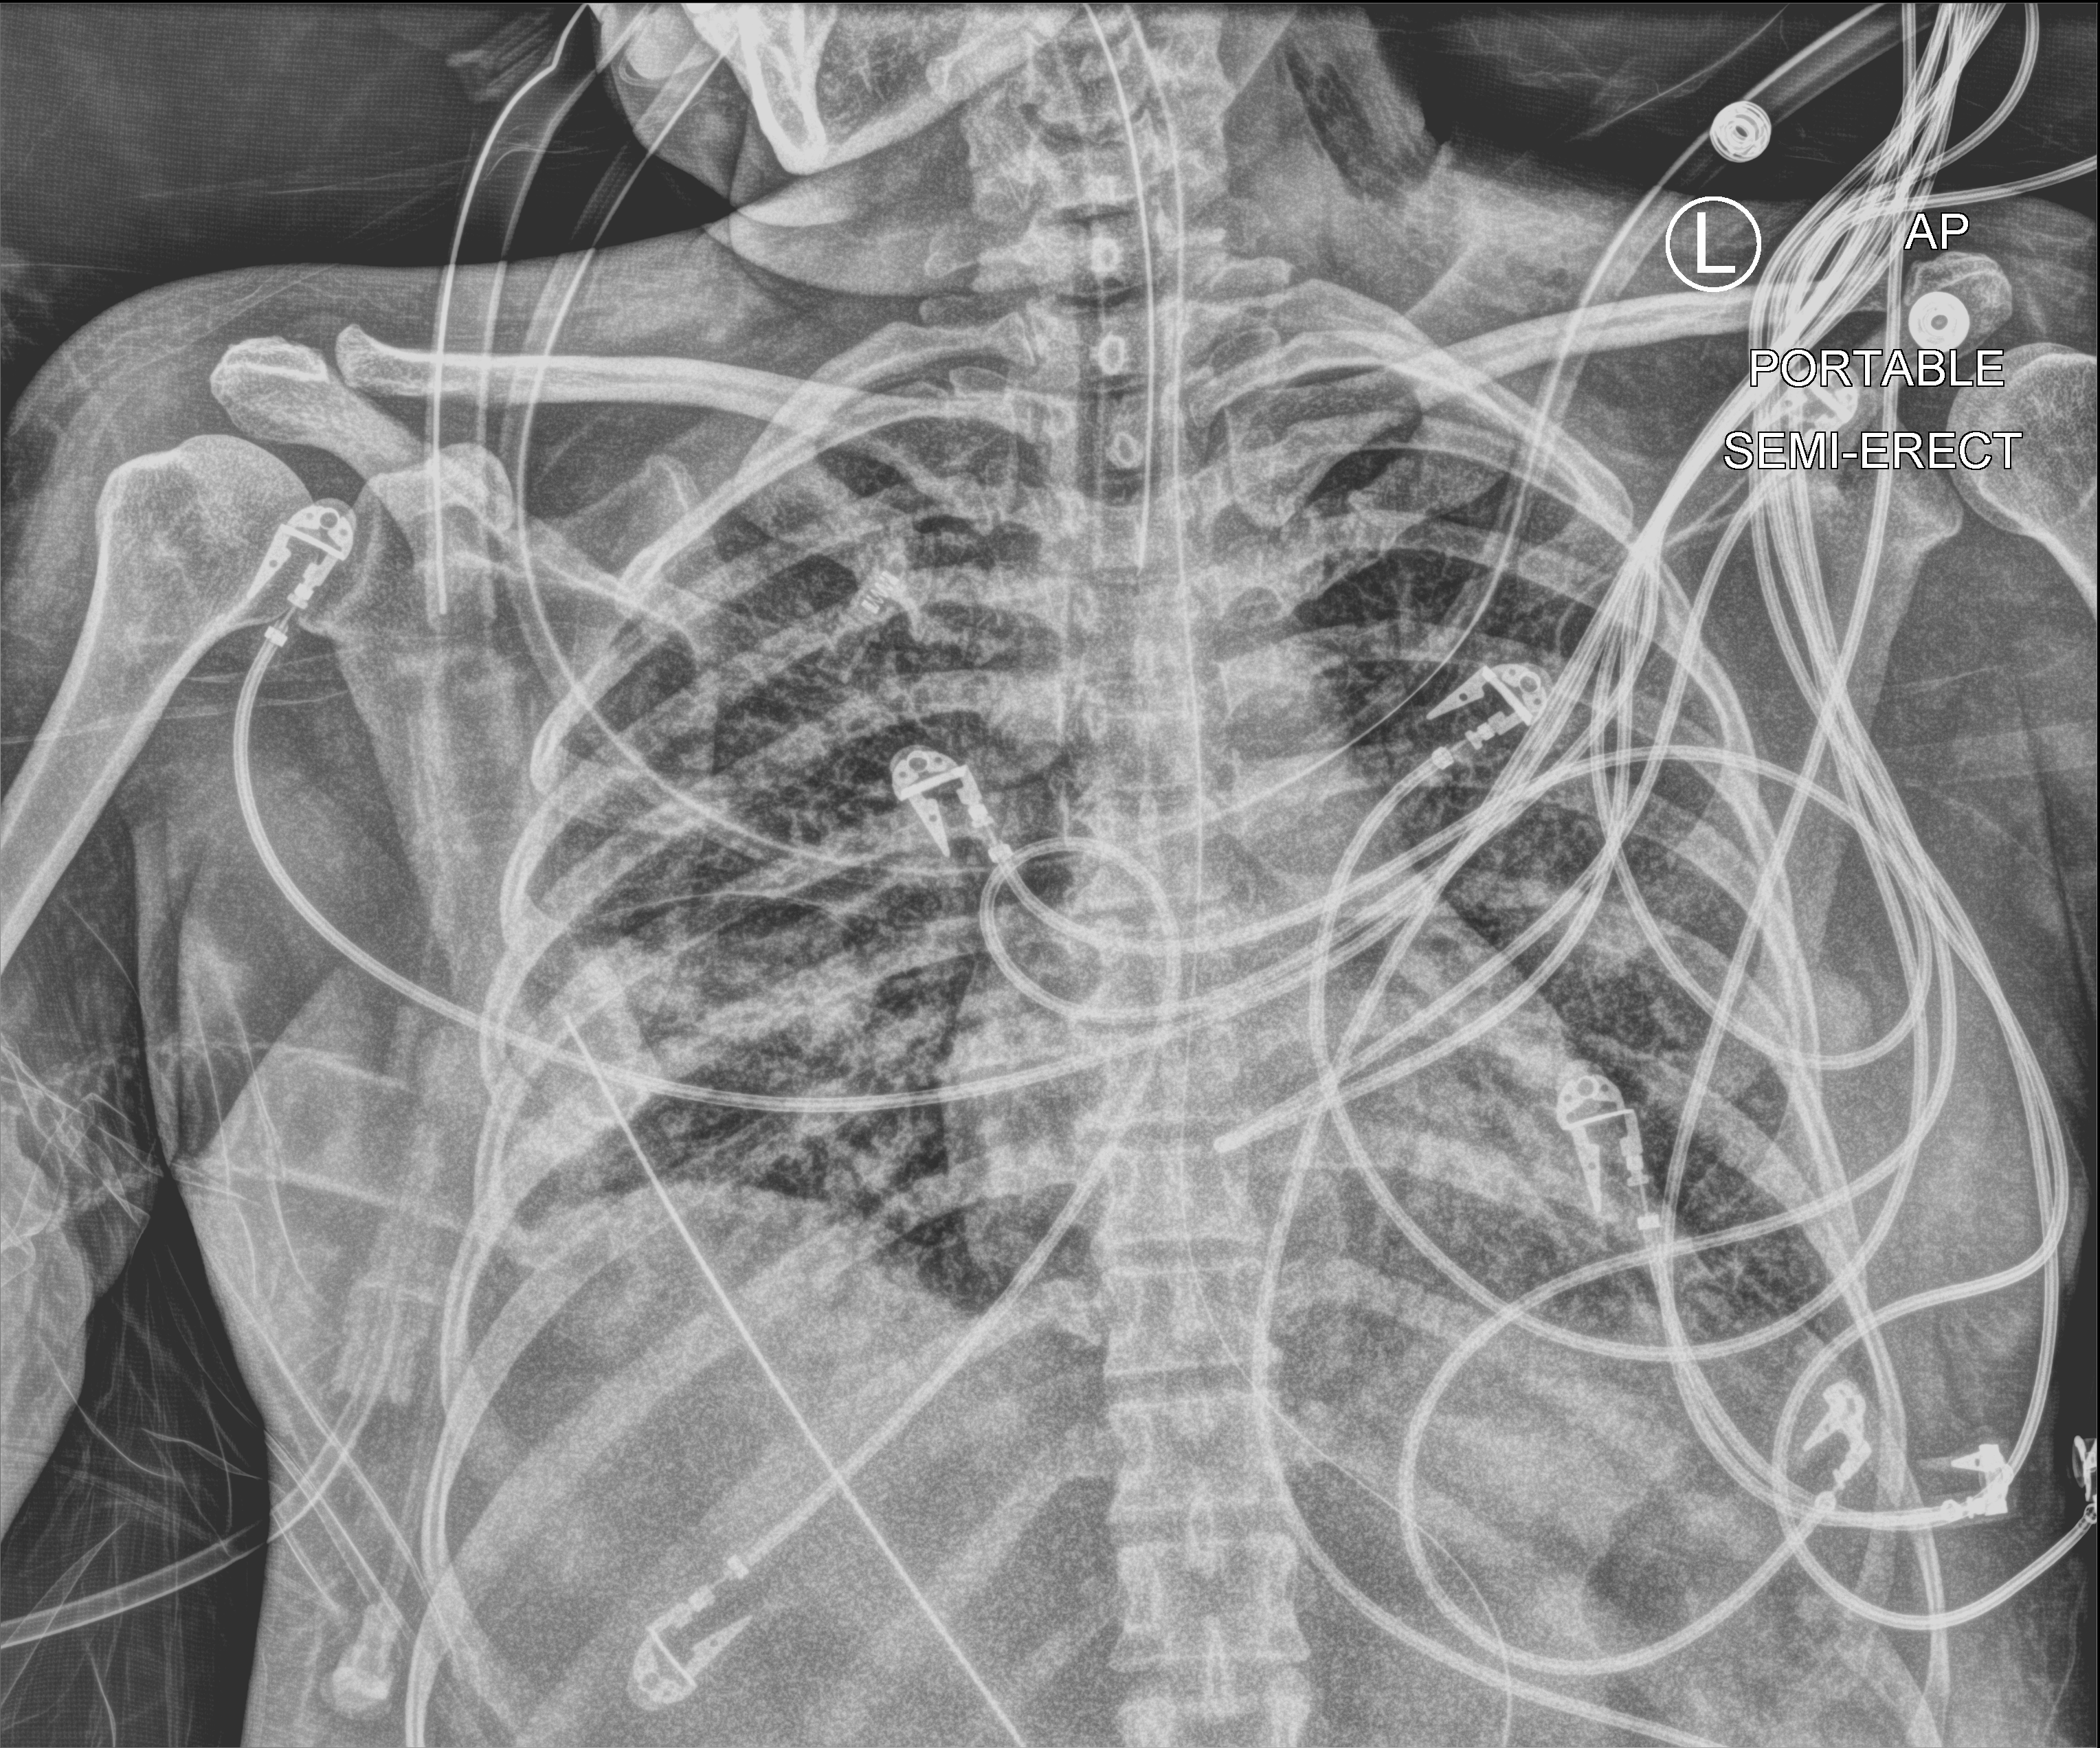
Bedside chest radiograph (computed radiography). Patient hospitalised with COVID-19; female, aged 18–59 years.
From the hospital-stay record, not from the radiograph (when in the stay this image was taken is not recorded): other chronic lung disease (admission record): no; admitted to intensive care during this hospital stay: yes.